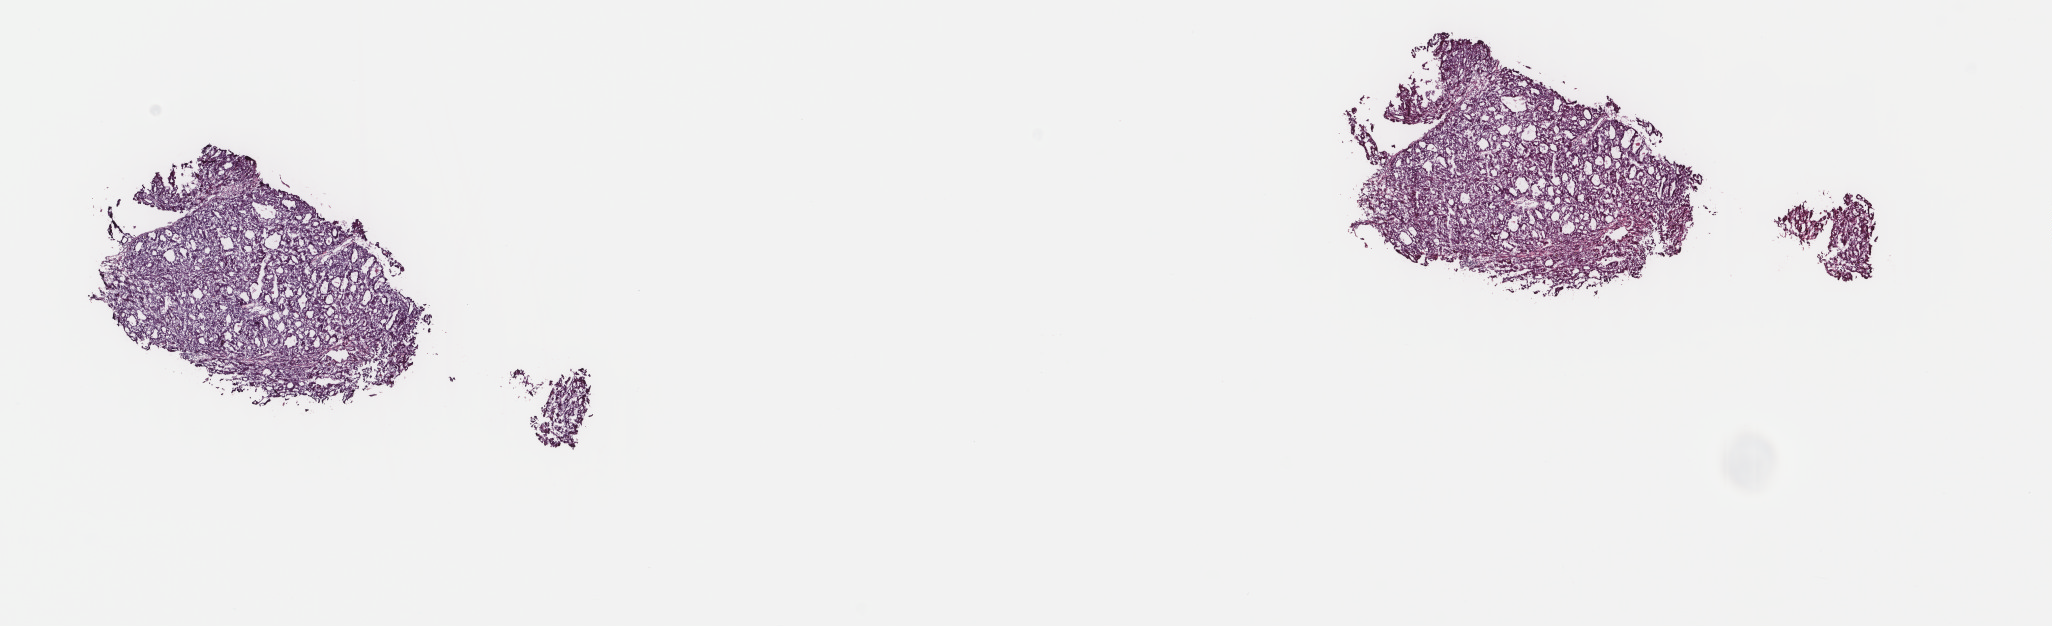
Whole-slide histology image, H&E, shown as a low-resolution overview of the whole scanned area (about 16.3 x 5.0 mm, slide scanned at 40x). Frozen section. Primary tumour sample from the liver. Male, age 52 years at initial diagnosis. Histologic grade: G2 (moderately differentiated). Composition of this section per pathologist review: tumour cells 100%, tumour nuclei 93%, normal cells 0%, stromal cells 0%, necrosis 0%. Infiltration values recorded for this section: lymphocyte infiltration 0%, monocyte infiltration 0%, neutrophil infiltration 0%.
• AJCC pathologic stage: II
• diagnosis: Hepatocellular carcinoma, NOS